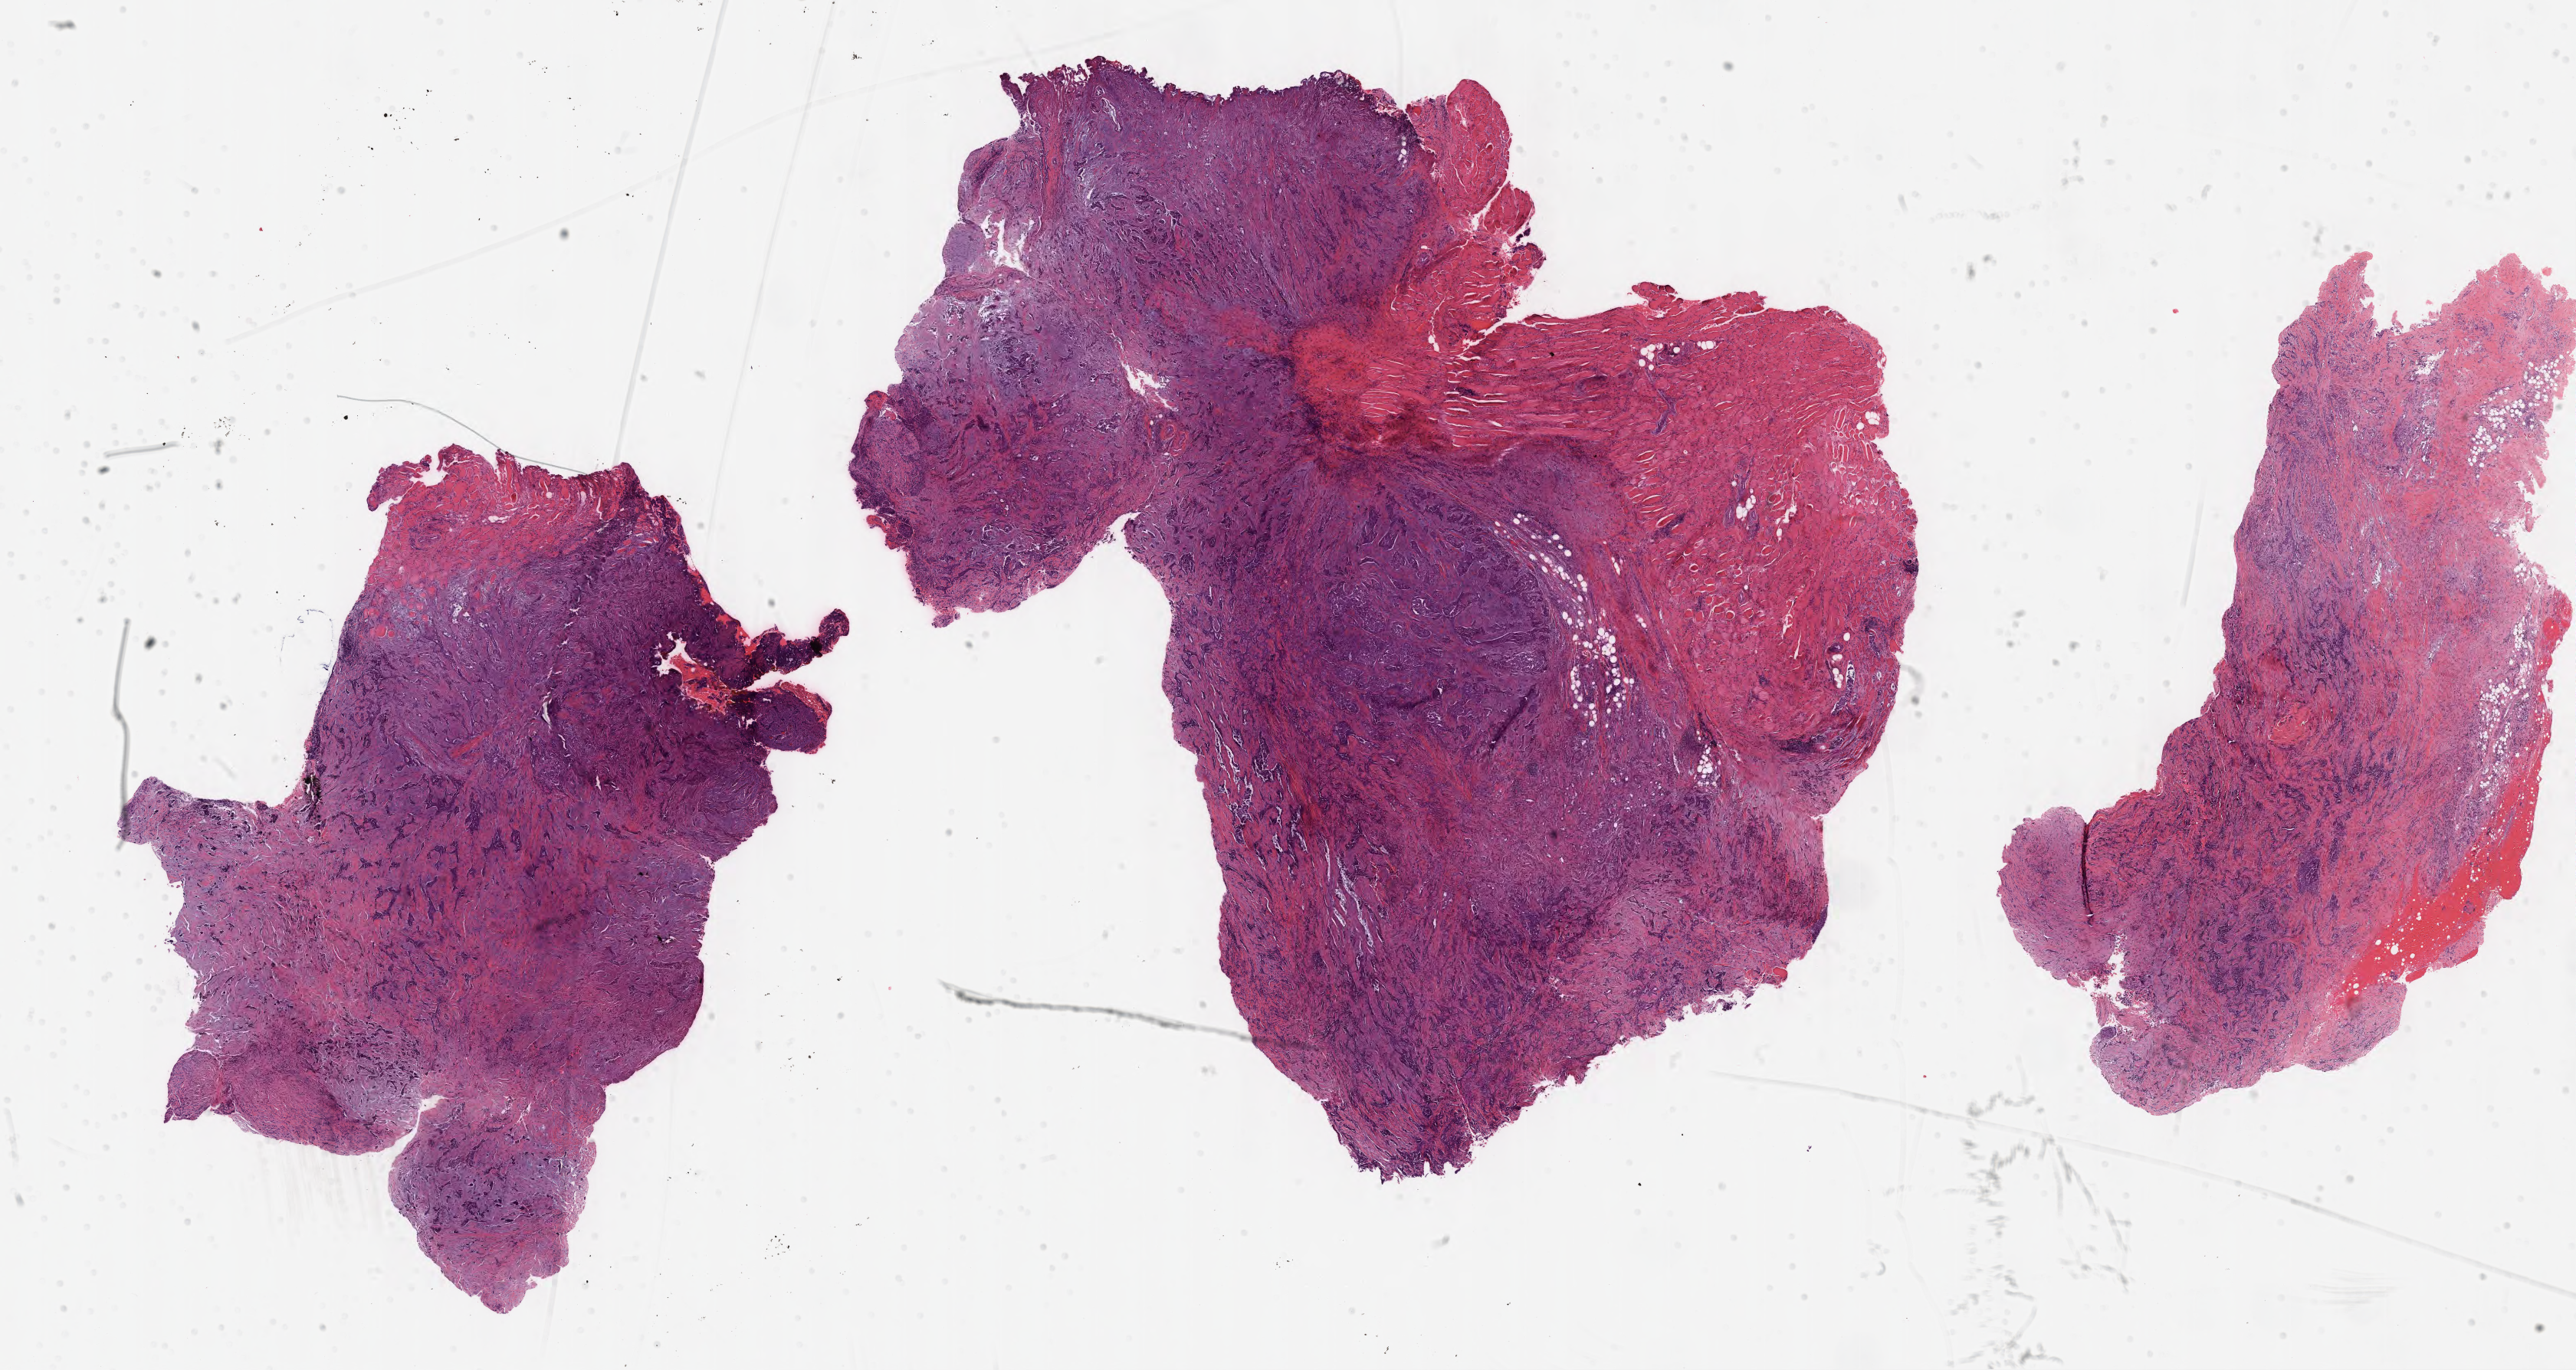
Whole-slide histology image, H&E, shown as a low-resolution overview of the whole scanned area (about 27.2 x 14.4 mm, from a 40x scan), formalin-fixed paraffin-embedded (FFPE) diagnostic section, sample: primary tumour, mesothelium. Patient: male, age at initial diagnosis 69 years.
Pathologic diagnosis: Epithelioid mesothelioma, malignant.